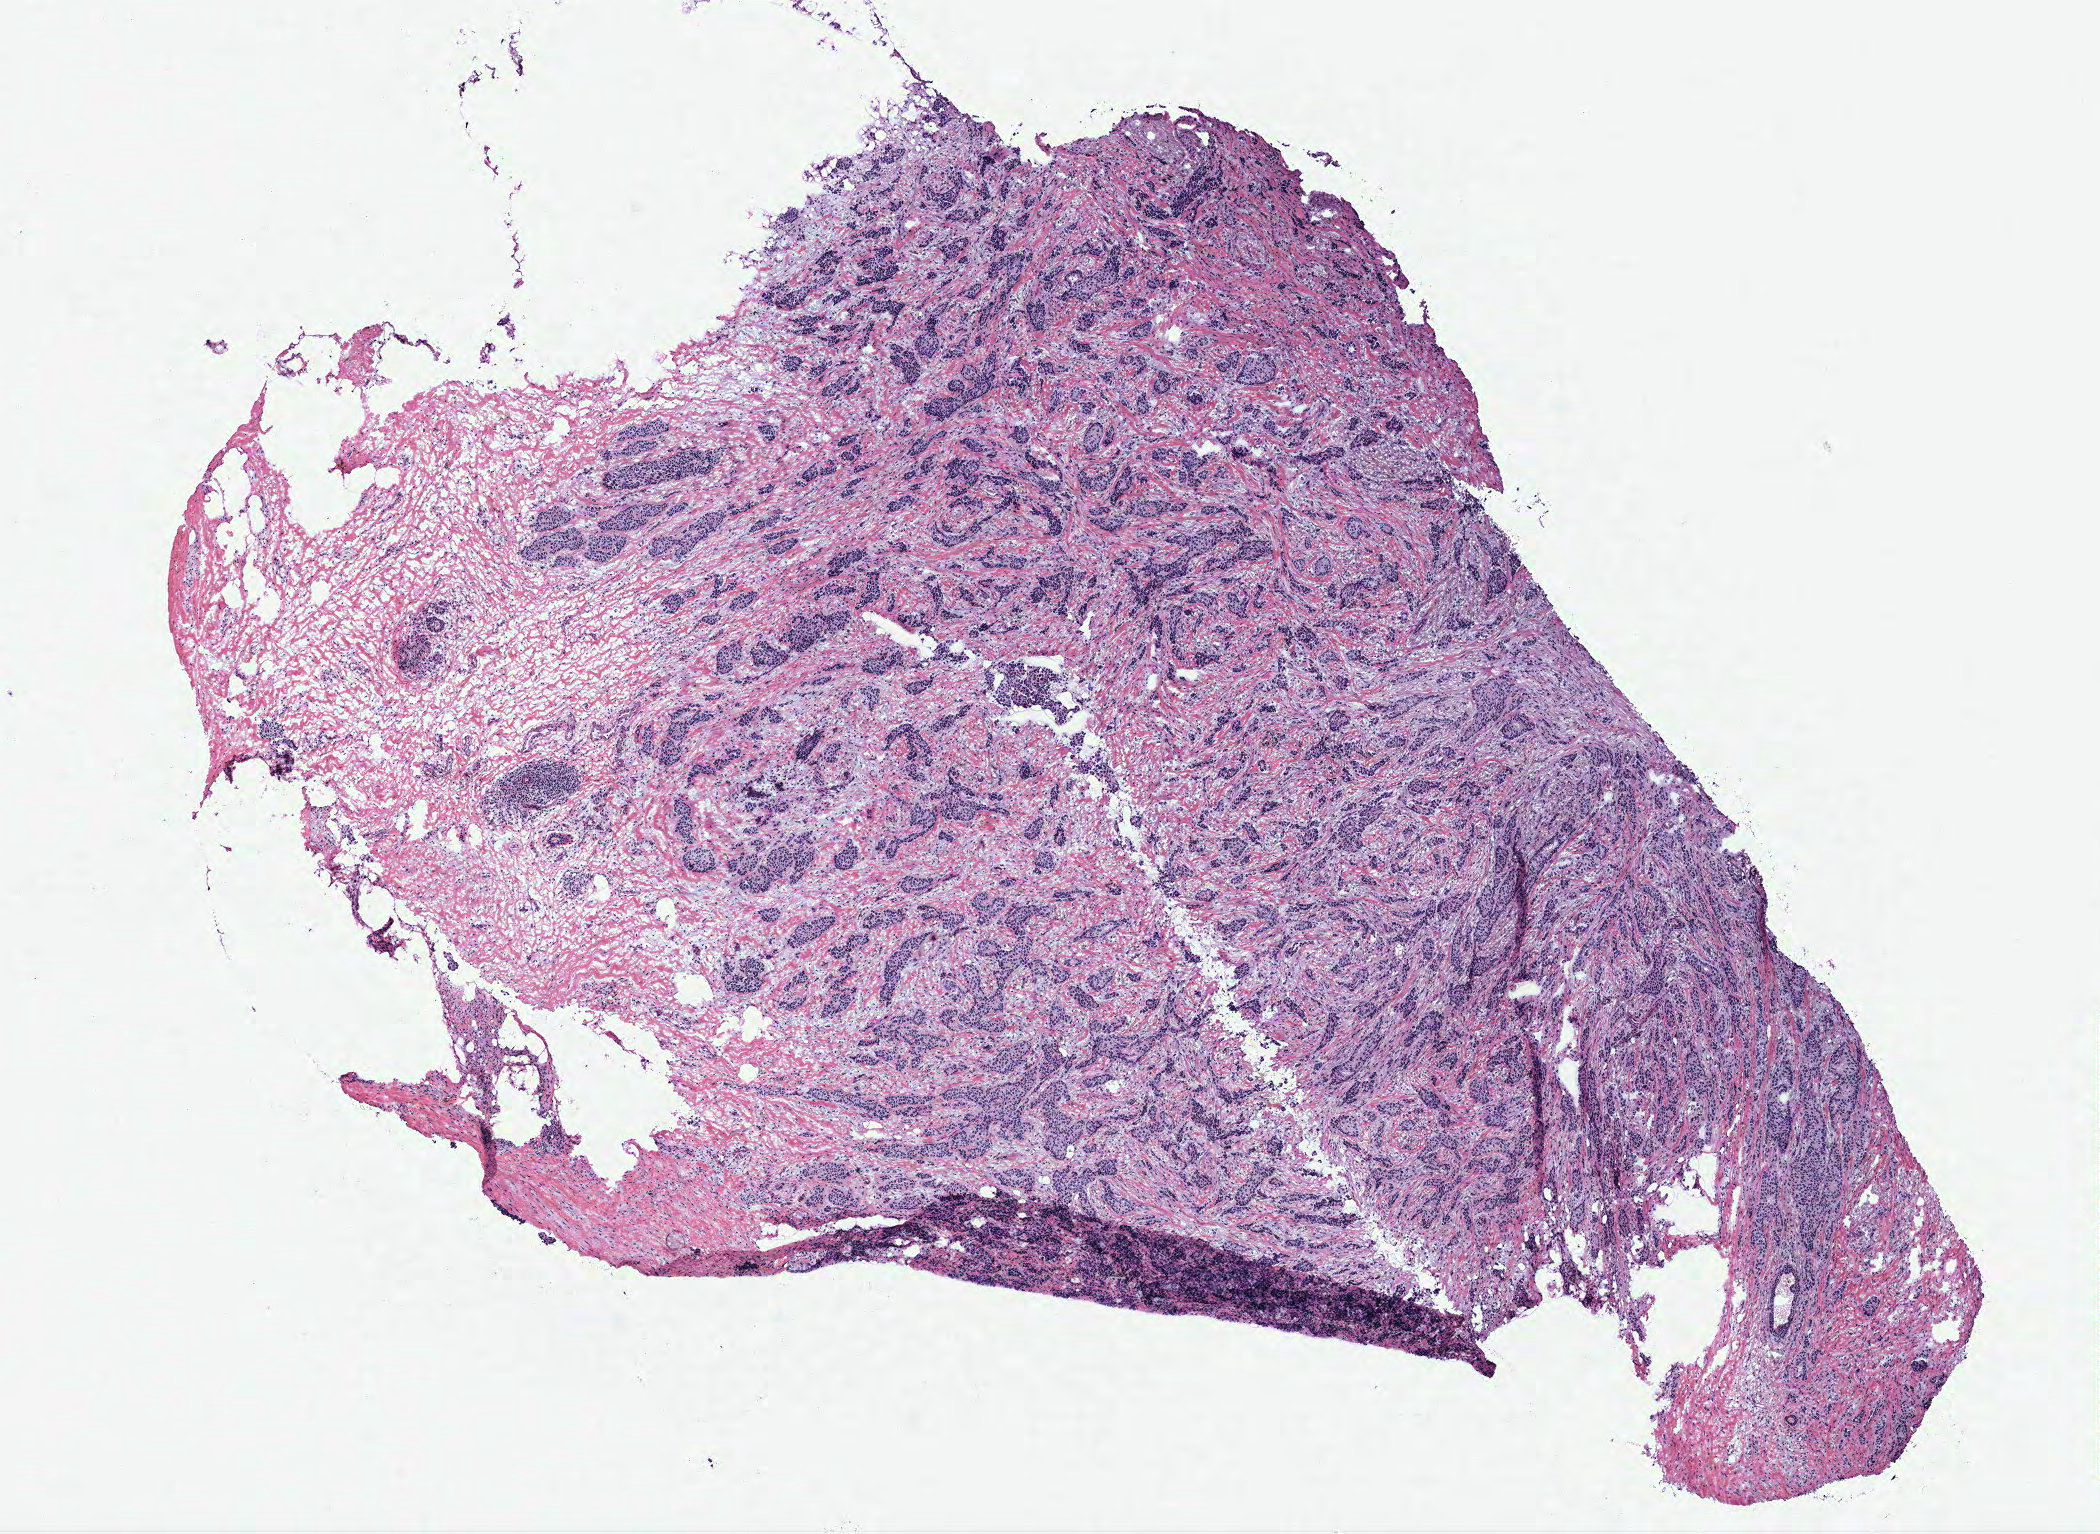
Digitized H&E tissue section (whole slide), a low-resolution overview of the entire scanned area, about 8.4 x 6.1 mm (slide scanned at 40x). Breast, tissue type not recorded.
• patient diagnosis (cohort enrolment): breast cancer (breast)